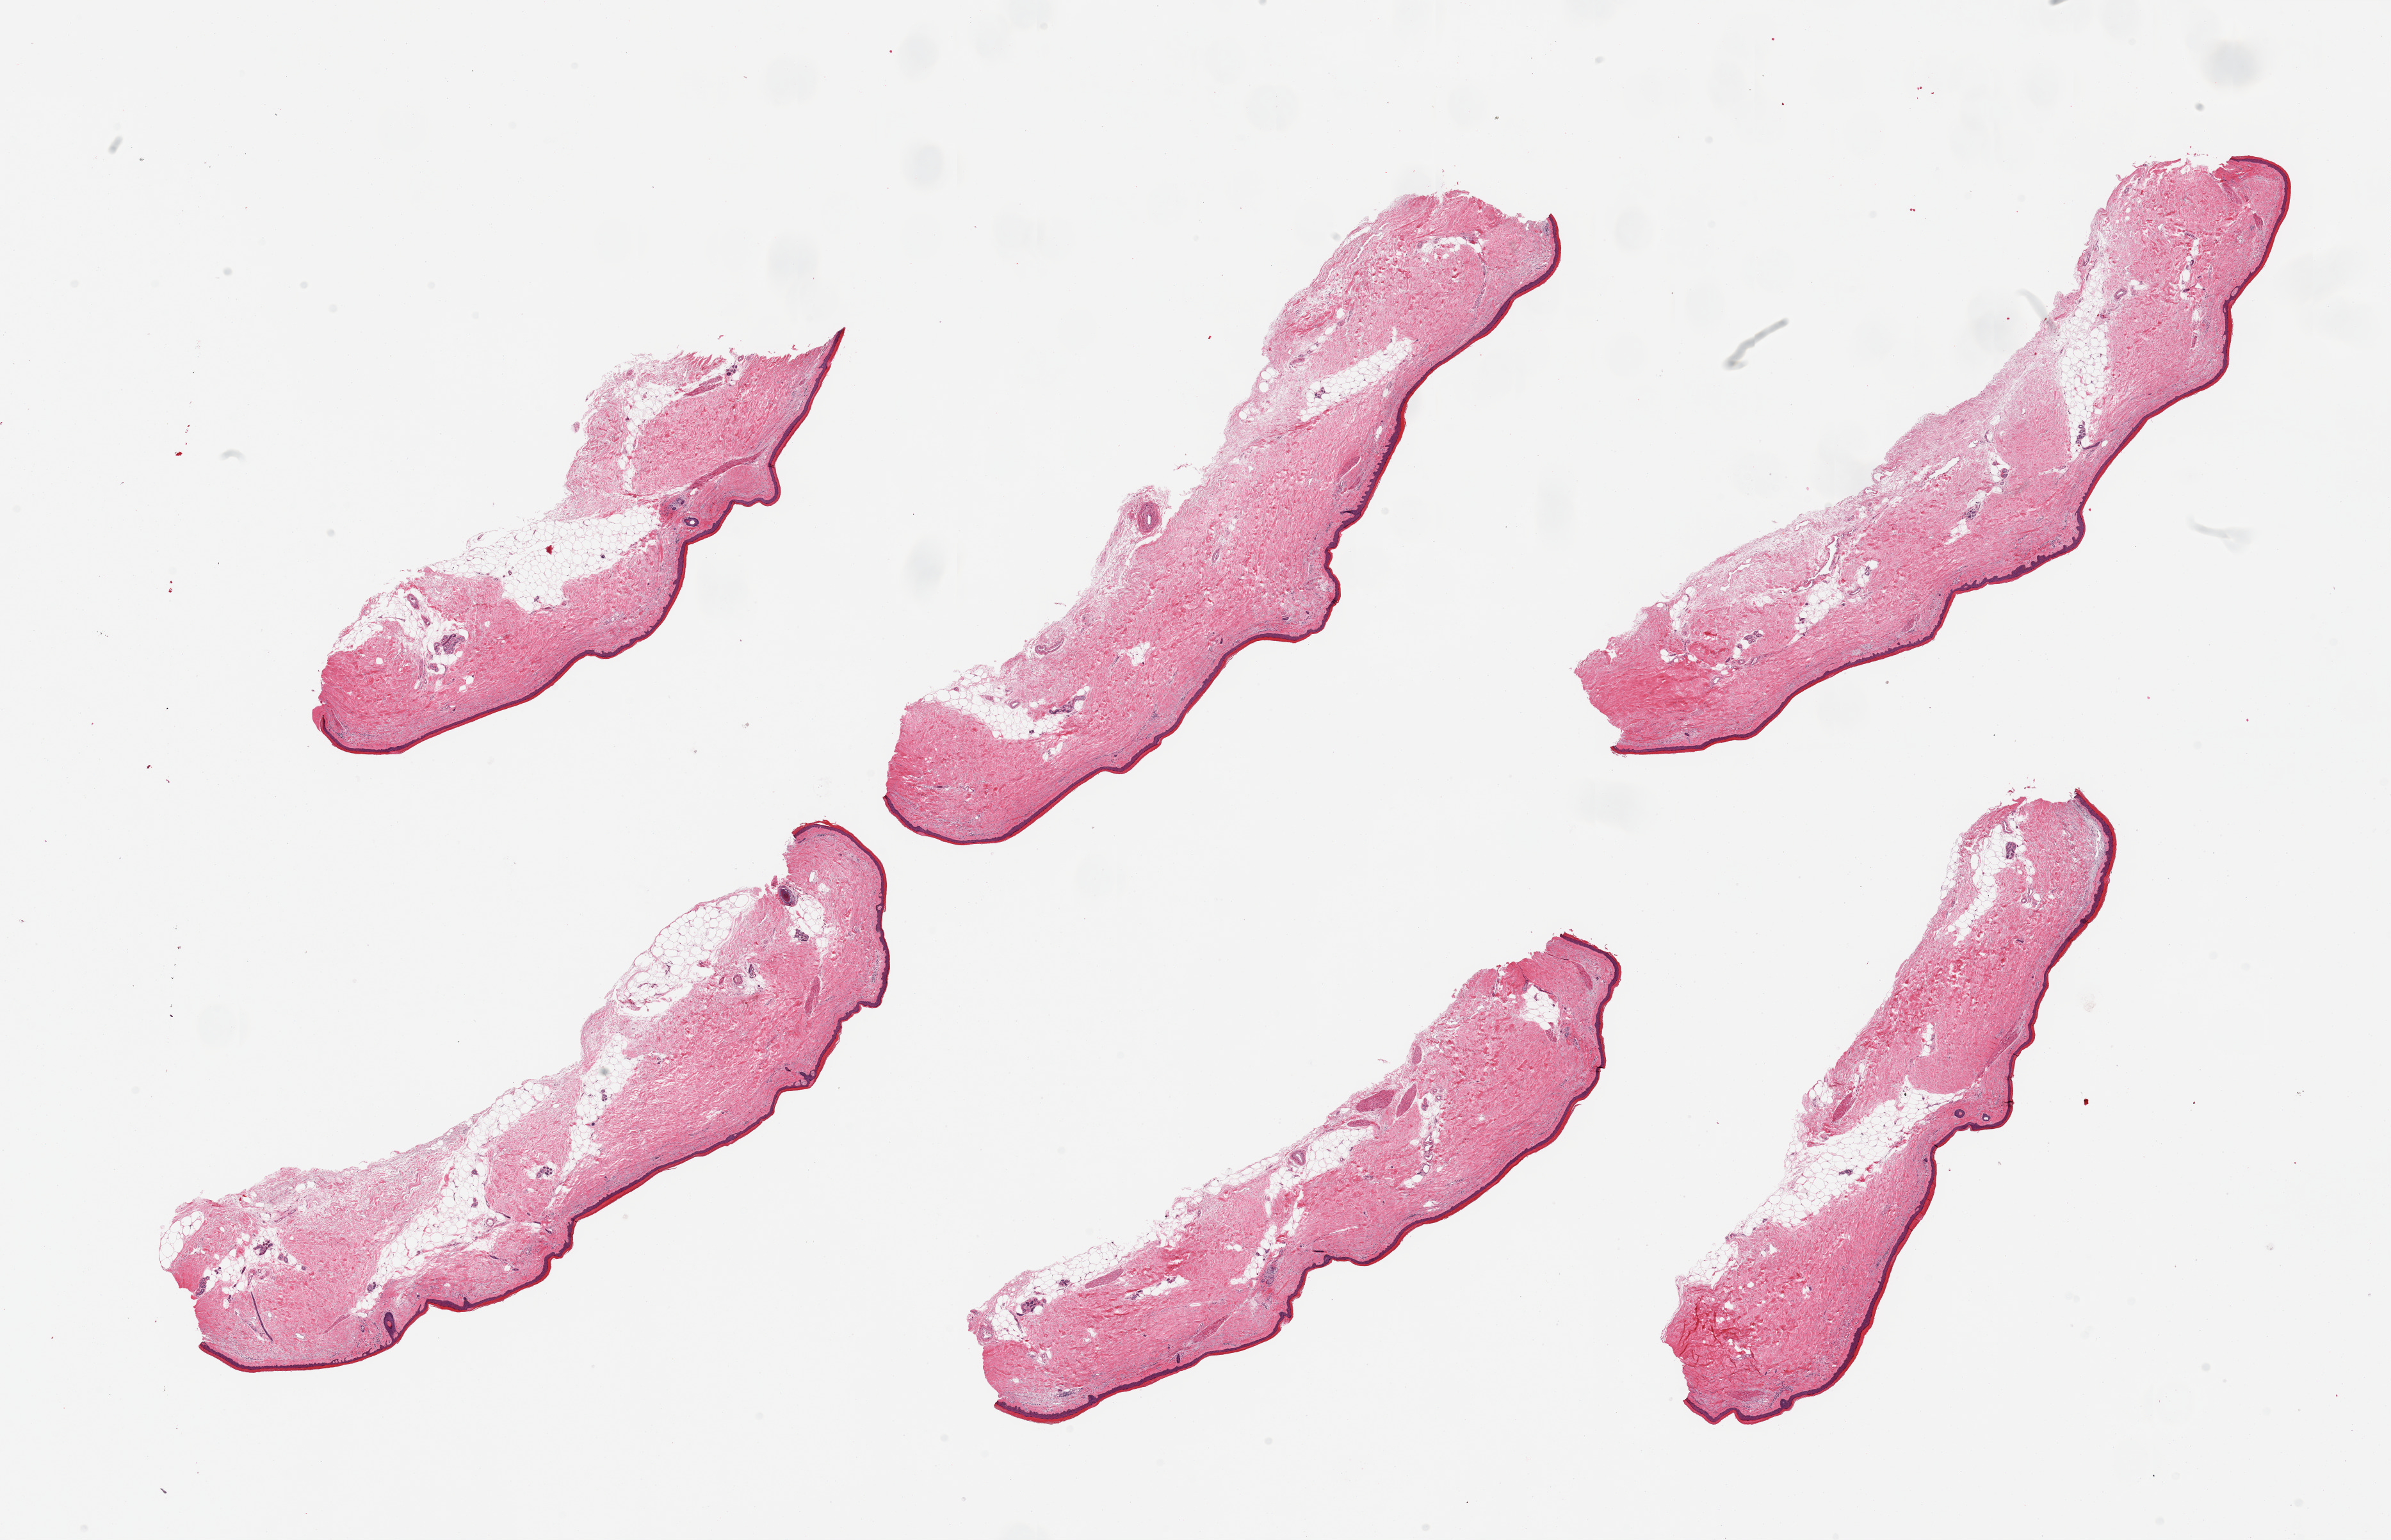
Digitized hematoxylin and eosin (H&E)-stained section — whole scanned area (about 29.5 x 19.0 mm, acquisition: 20x scan) shown as a low-resolution overview, PAXgene-fixed paraffin-embedded (PFPE) section, sampled site (target tissue): skin of lower leg, donor tissue sample. Donor sex: female.
* reviewer comment on this tissue sample: 6 pieces, focal dermal fat up to ~1mm, squamous epithelium is ~40 microns